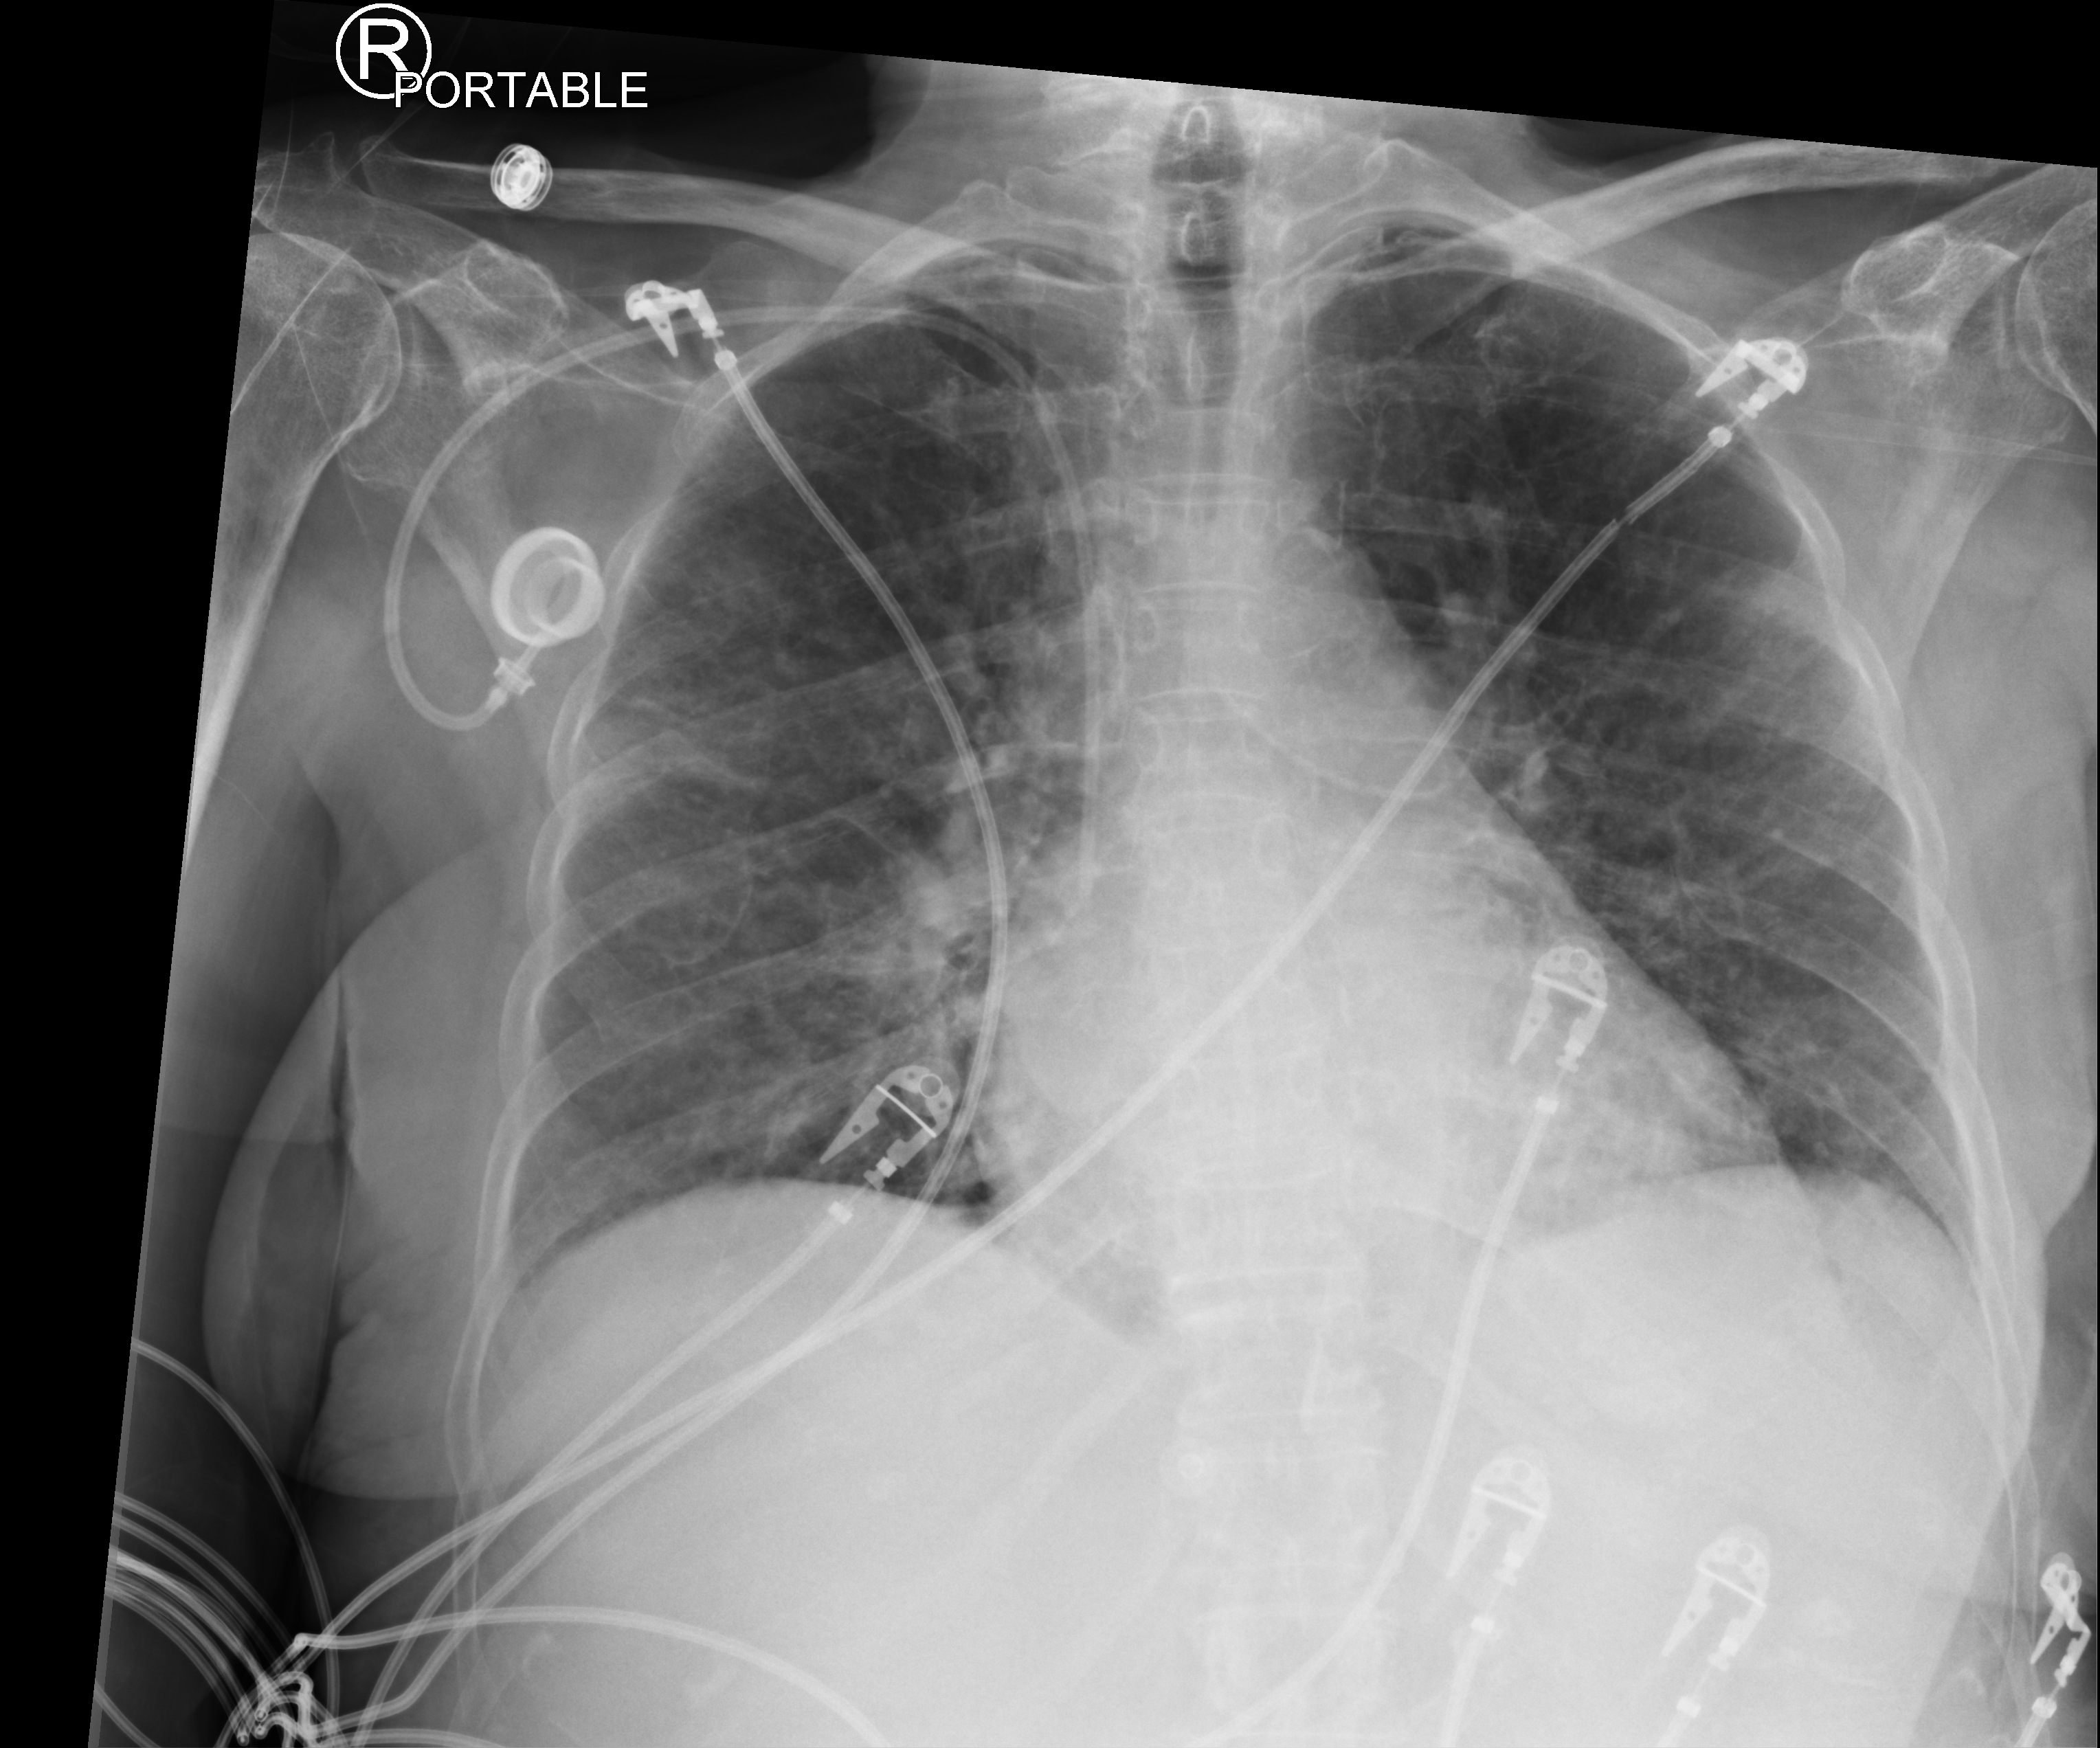
Bedside chest radiograph (computed radiography); anteroposterior (AP) projection. Female patient hospitalised with COVID-19, age 75–90 years.
Admission-level facts for this patient (not findings on this image; timing relative to this image not recorded): admitted to intensive care during this hospital stay: yes; mechanically ventilated during this hospital stay: no; length of hospital stay: 7 days.